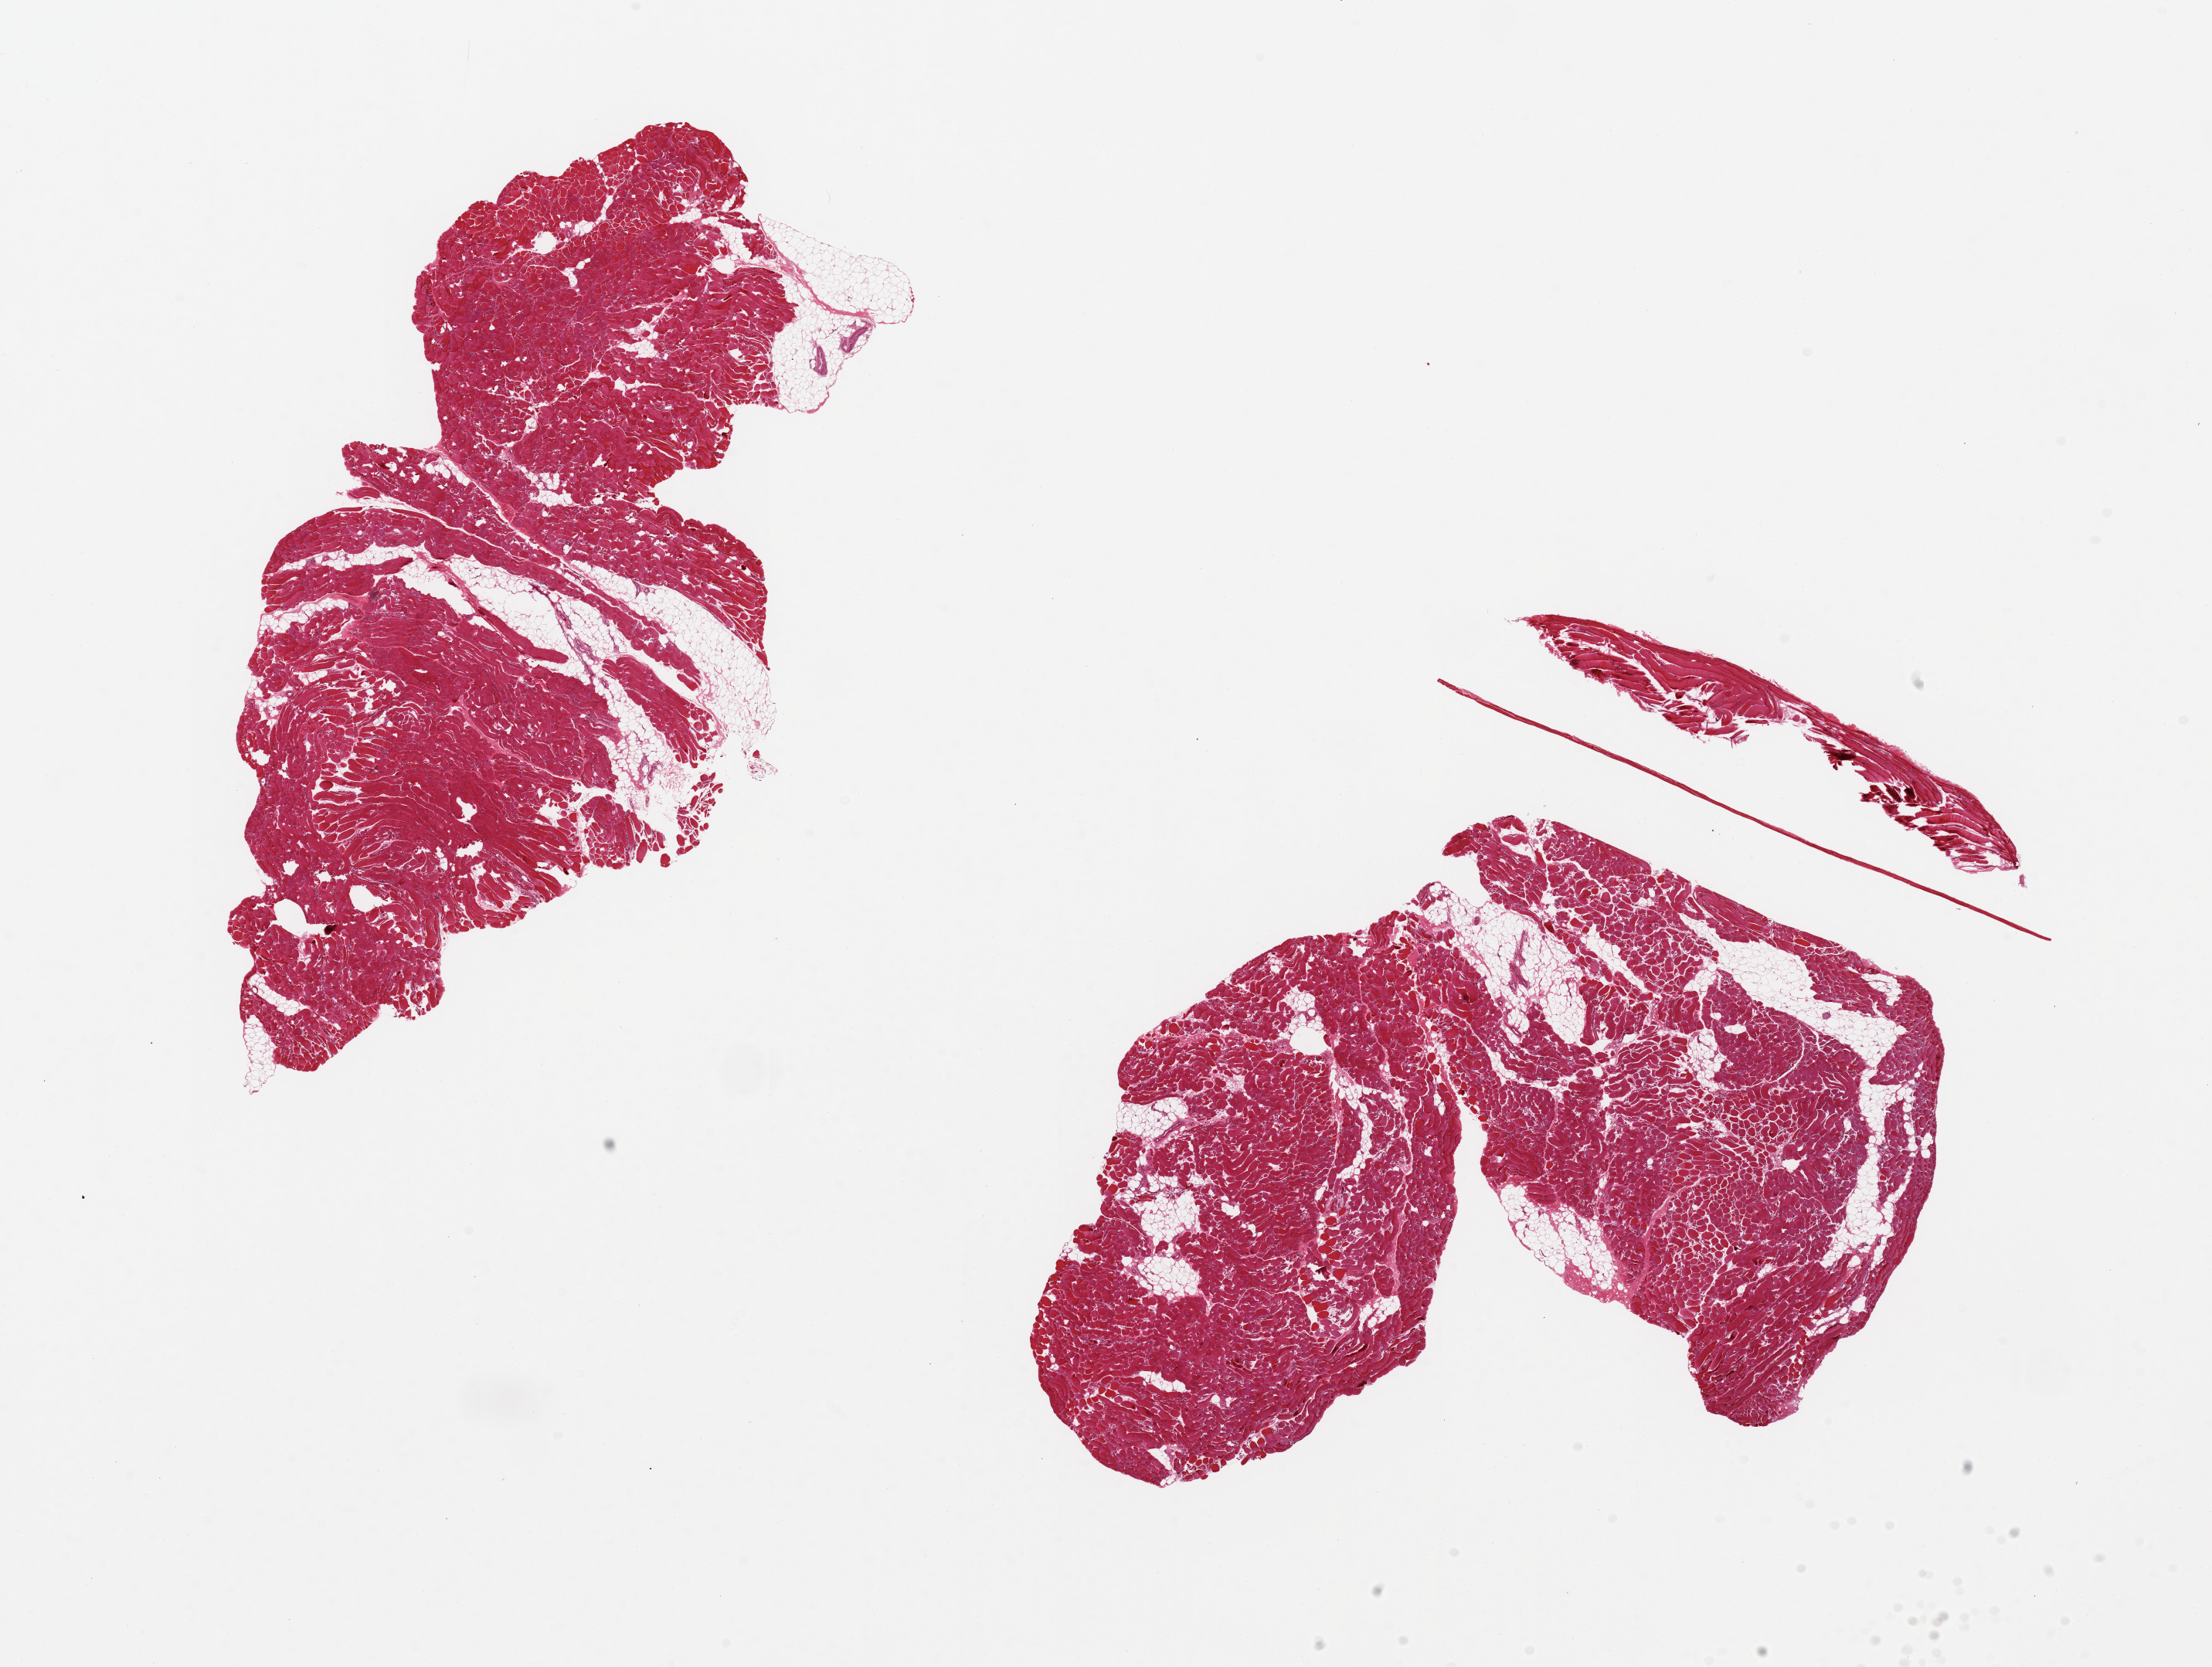
Whole-slide image, haematoxylin and eosin stain, brightfield — whole scanned area (about 22.6 x 17.1 mm, slide scanned at 20x) shown as a low-resolution overview. PAXgene-fixed, paraffin-embedded tissue. Sampled site (target tissue): skeletal muscle. Tissue donor sample.
Pathologist's review note for this sample: 2 pieces ~10x5mm. ~15-20% interstitial fat.